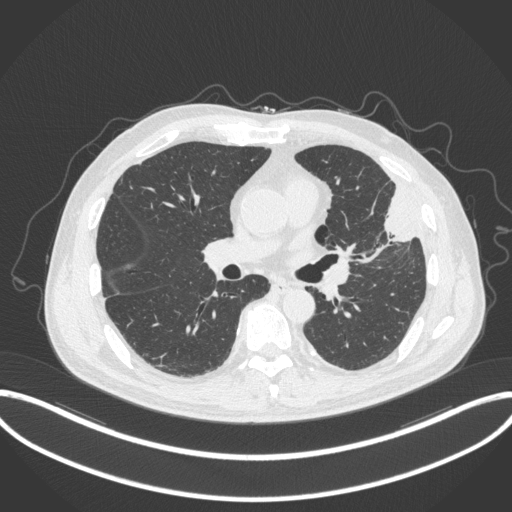
Chest CT, one axial slice; slice 181 of 382 in the series (ordered by position); reconstruction kernel B31f; 120 kVp; lung window (W 1500 / L -600 HU); 1 mm slice thickness; 512 × 512 image matrix, field of view 415 × 415 mm. Patient: male, 64 years. Case-level facts recorded for this patient, not image findings: clinical TNM (as recorded): T4 N1 M0; histopathological grade: G3.
Outlined on this slice (bounding box drawn by a radiologist):
- lung tumour (recorded histology: adenocarcinoma): bounding box [x1, y1, x2, y2] px = [376, 182, 421, 247]